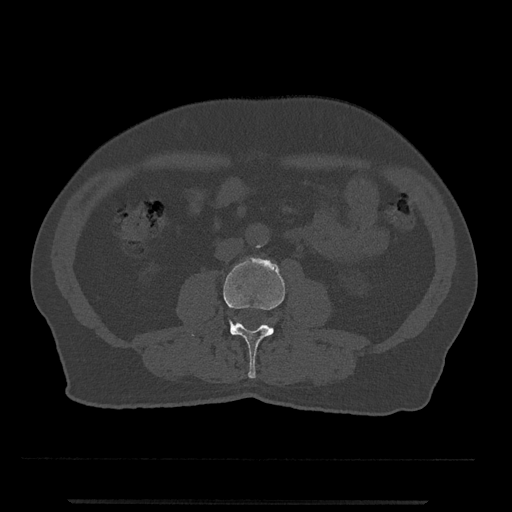
CT including the spine, one axial slice. Slice 192 of 797 in the series (ordered by position). Reconstruction kernel Br40s/3. Bone window (W 1800 / L 400 HU). 512 × 512 image matrix. Patient: male, 63 years. Case-level facts recorded for this patient, not image findings: primary cancer: prostate.
Structures marked on this image (semi-automatic segmentation, software-assisted and operator-edited):
- L3 vertebra: bounding box [x1, y1, x2, y2] px = [191, 257, 285, 379]